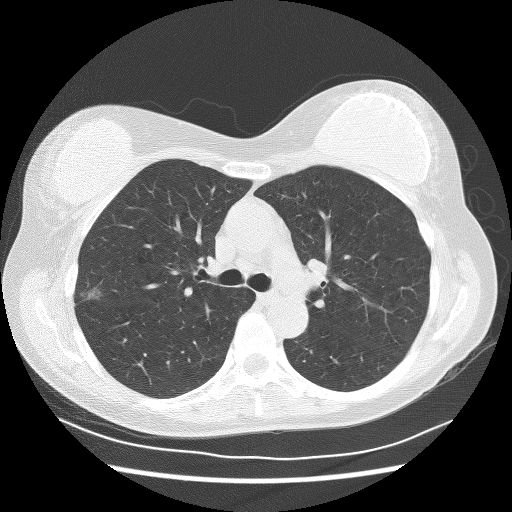
Low-dose screening chest CT, axial slice; first (baseline) screen; lung window (W 1500 / L -600 HU); slice 83 of 253 in the series. Female, age 58 years at enrolment.
Lesion marked by an expert reader, bounding box <63,271,117,312> (left, top, right, bottom; pixels). The screening reader recorded 2 non-calcified nodules or masses ≥4 mm on this exam (right upper lobe, right upper lobe); which of them this box marks is not recorded. Official screen result: positive, change unspecified: nodule(s) >= 4 mm or enlarging nodule(s), mass(es), or other non-specific abnormalities suspicious for lung cancer. Participant outcome: lung cancer diagnosed 510 days after this screen (after the second annual screen) — bronchiolo-alveolar adenocarcinoma, NOS, right upper lobe, well differentiated (G1), stage IA (AJCC 6th edition).